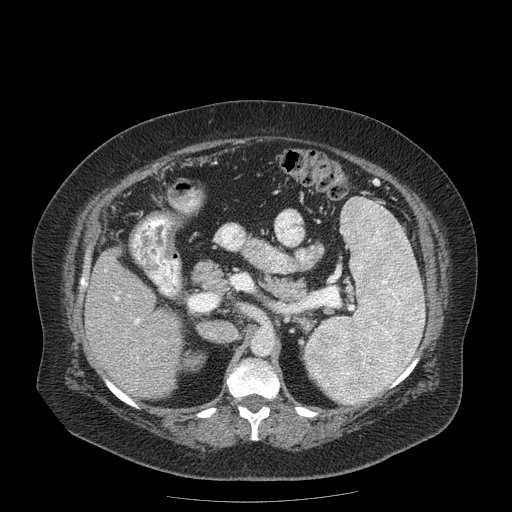
Contrast-enhanced abdominal CT (liver protocol), one axial slice. Slice 89 of 204 in the series (ordered by position). 120 kVp. Soft-tissue window (W 400 / L 40 HU). 2.5 mm slice thickness. 512 × 512 image matrix, field of view 440 × 440 mm. From the clinical record (not read from this slice): diagnosis: hepatocellular carcinoma (patient treated with transarterial chemoembolisation; whether this scan precedes or follows treatment is not stated here); TNM stage (as recorded): Stage-IIIB; Child-Pugh class: A.
Outlined on this slice (semi-automatic segmentation, software-assisted and operator-edited):
- liver parenchyma outside the tumour (the mass and vessels are separate outlines, so this box may not span the whole liver): box from (x=86, y=250) to (x=184, y=398) px
- liver vessels: (x=105, y=270)–(x=140, y=325)